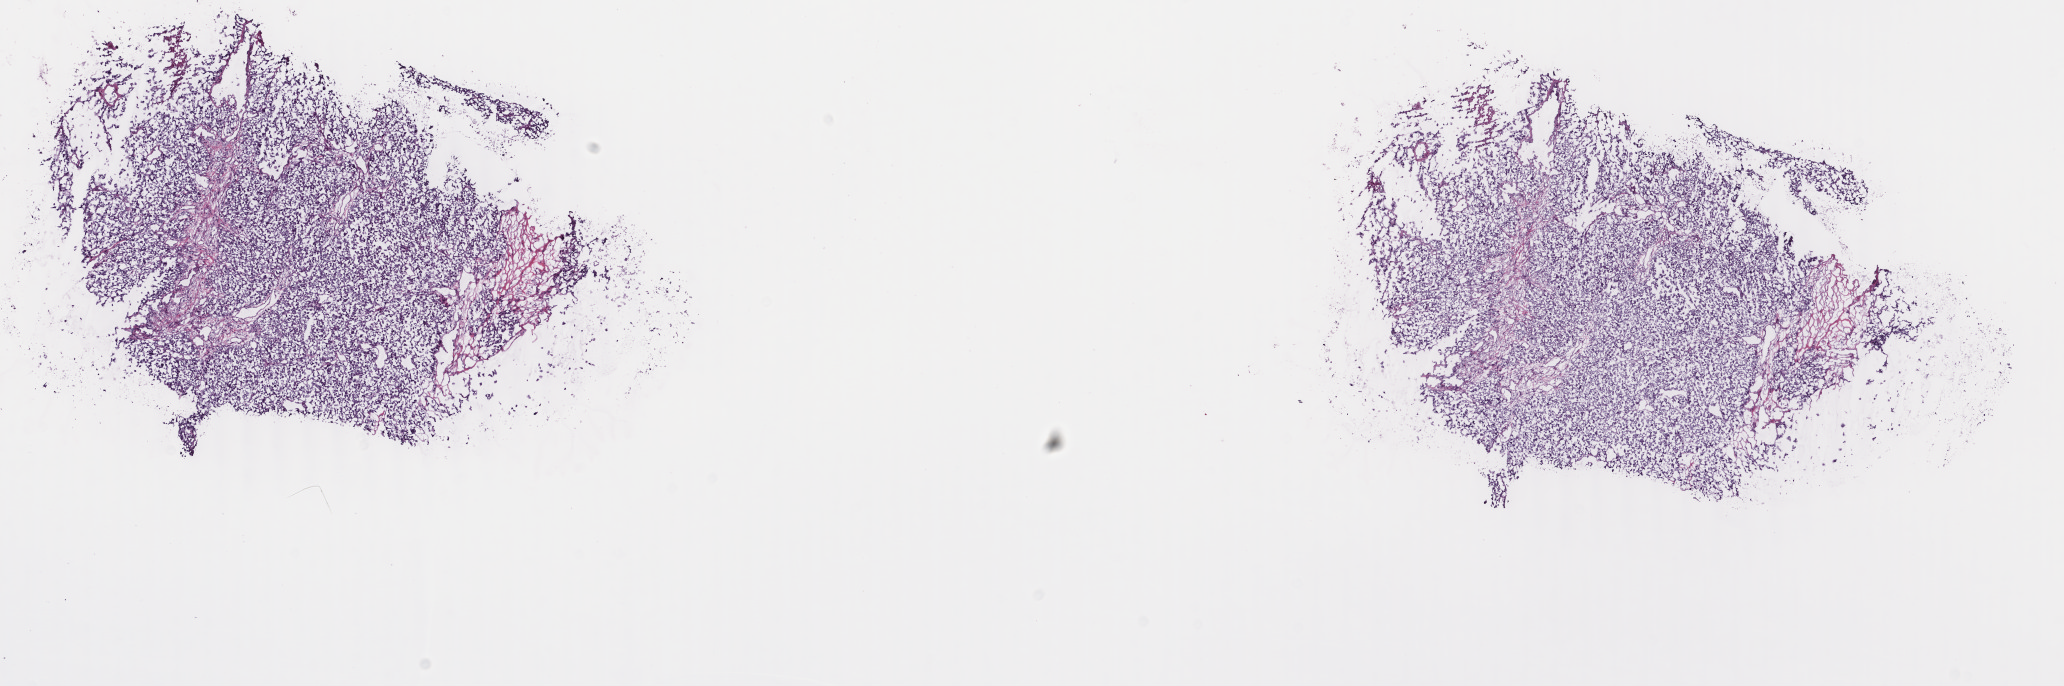
Whole-slide histology image, H&E-stained, low-resolution overview of the scanned area, about 16.4 x 5.5 mm (acquisition: 40x scan). Frozen section from the top of the tissue portion. Metastatic tumour sample, sampled site not recorded. Female, age 63 years at initial diagnosis. Composition of this section per pathologist review: tumour cells 100%, tumour nuclei 90%, normal cells 0%, stromal cells 0%, necrosis 0%. Infiltration values recorded for this section: lymphocyte infiltration 0%, monocyte infiltration 0%, neutrophil infiltration 0%.
- this section: metastatic tumour tissue
- patient diagnosis: Malignant melanoma, NOS